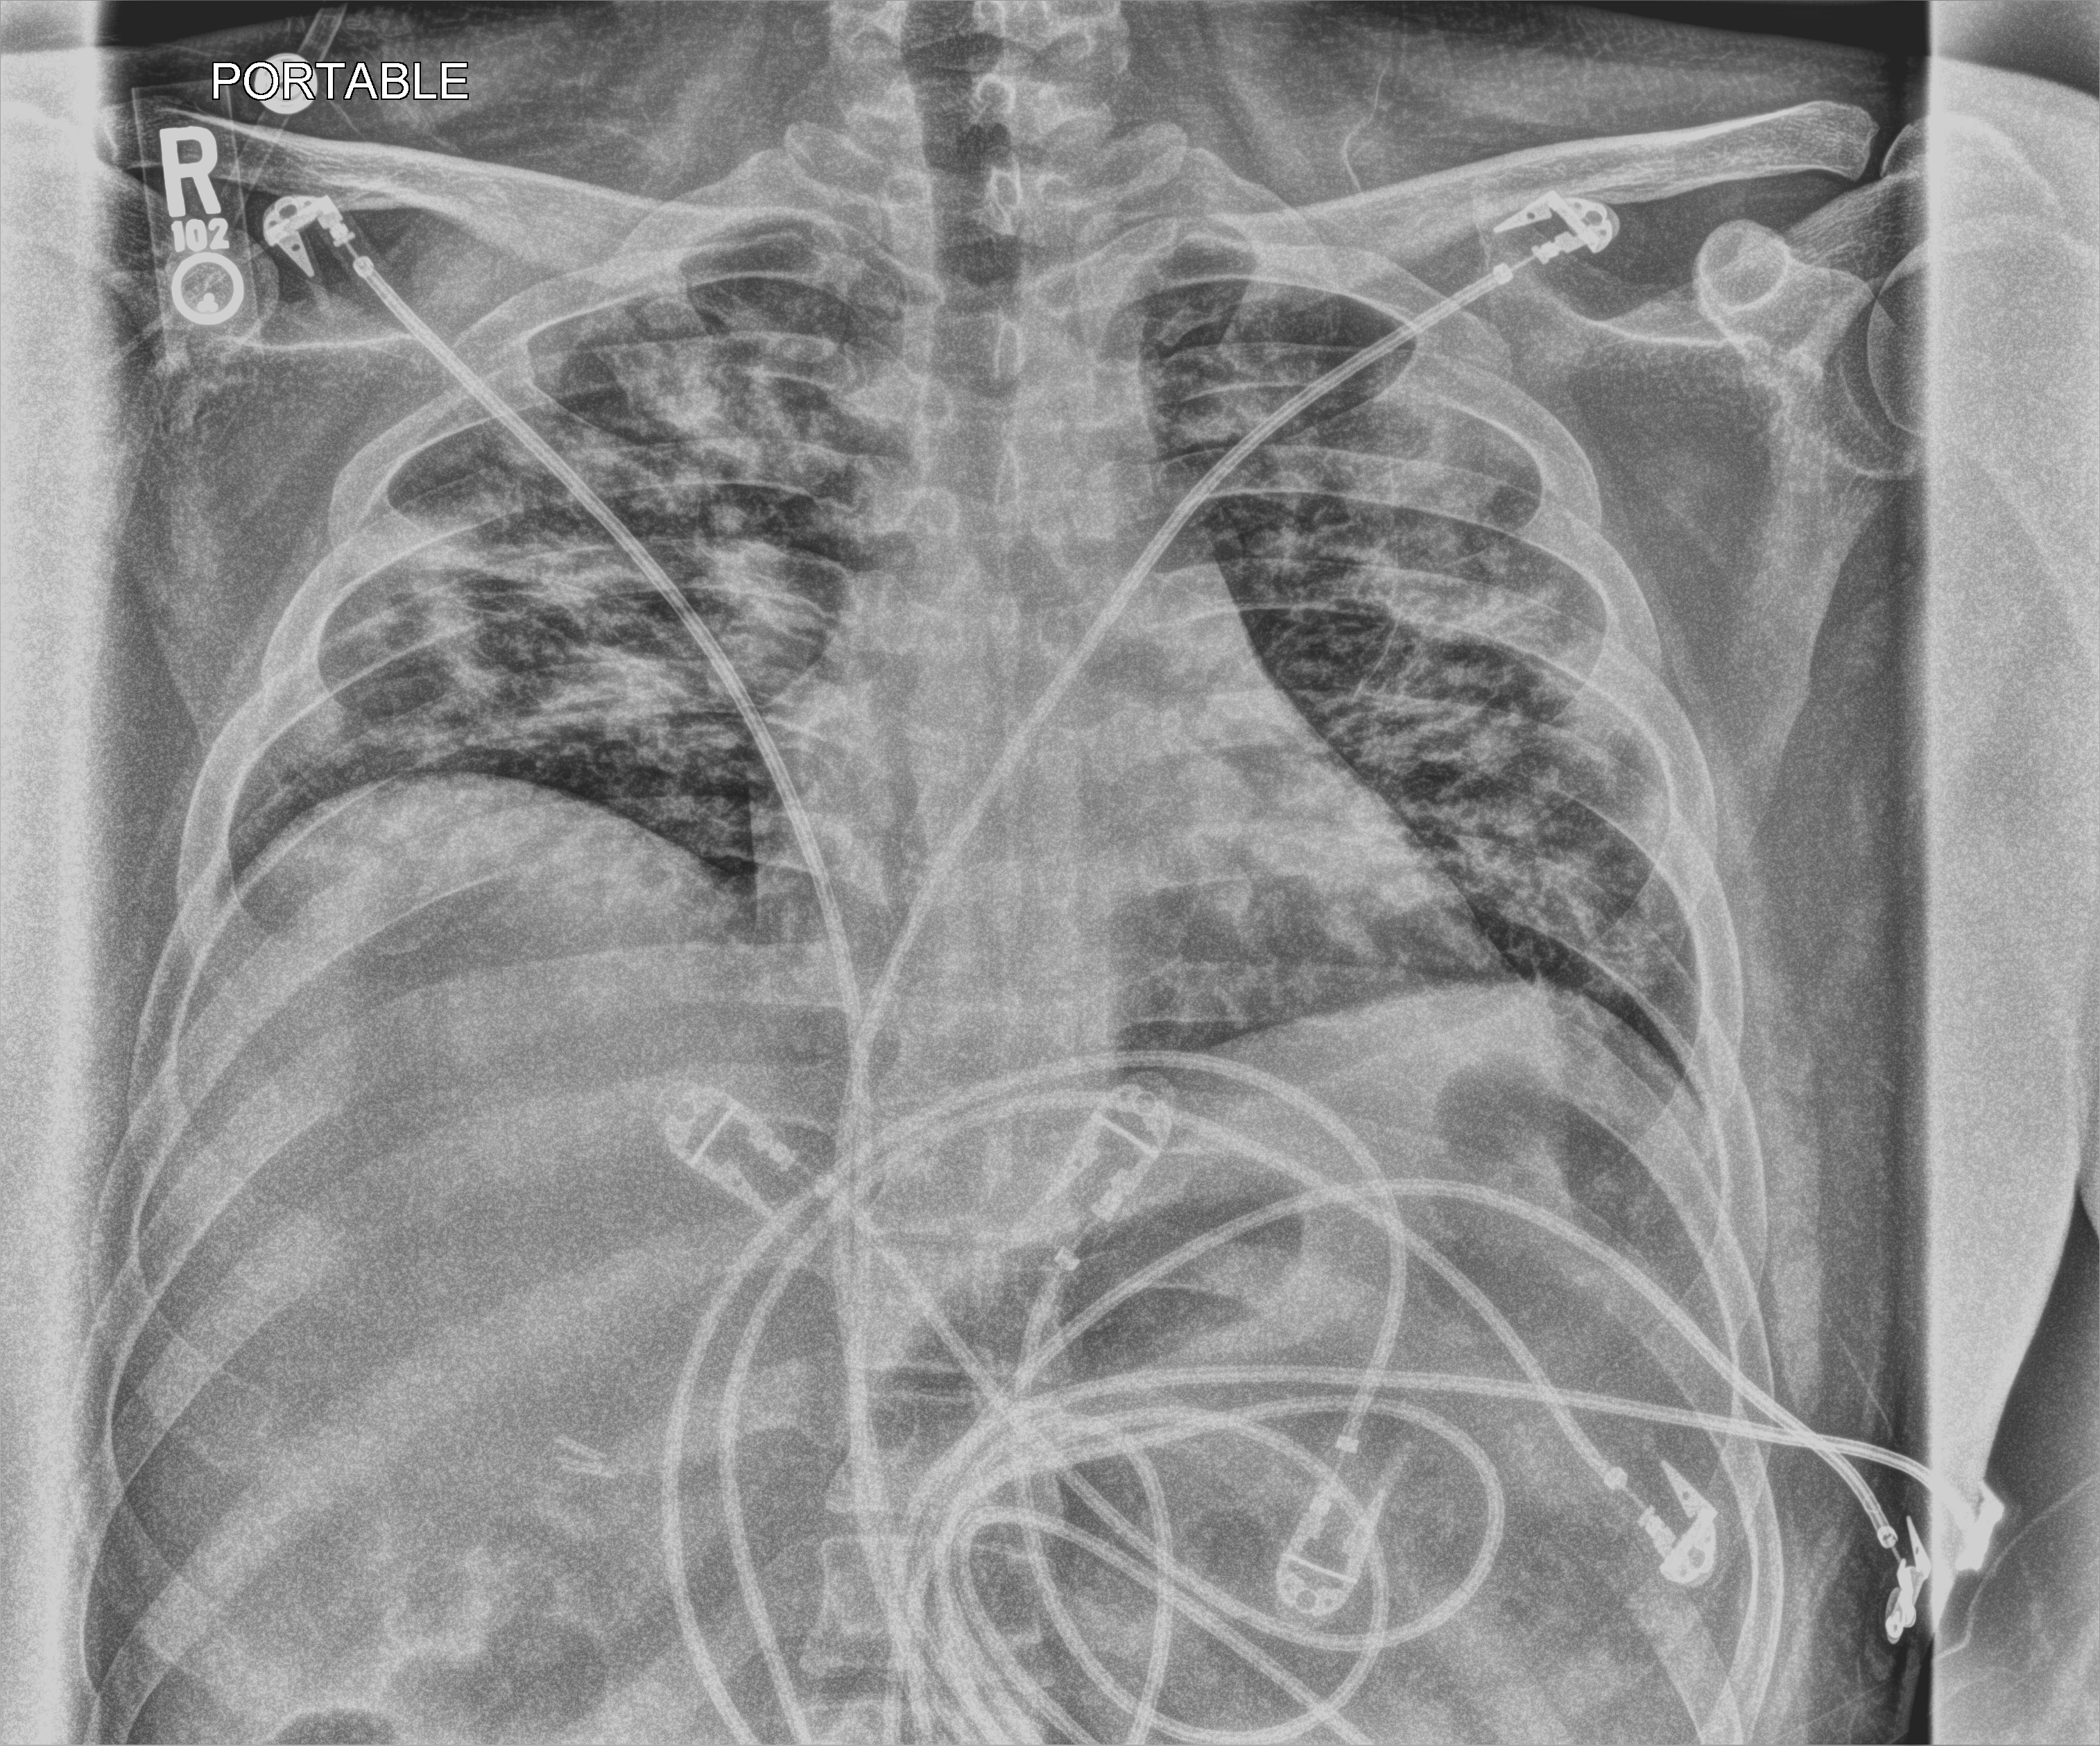
Portable chest radiograph, anteroposterior (AP) projection. Male patient hospitalised with COVID-19, age 18–59 years.
Admission-level facts for this patient (not findings on this image; timing relative to this image not recorded): mechanically ventilated during this hospital stay: yes; admitted to intensive care during this hospital stay: yes.